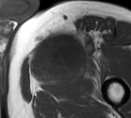
MRI of an extremity soft-tissue mass, one axial slice. Slice 51 of 55 in the series (ordered by position). MR volume resampled by the dataset authors to the PET/CT grid (not the native acquisition matrix). 131 × 118 image matrix. Male patient. From the clinical record (not read from this slice): histological type: pleiomorphic liposarcoma; grade: high; site of the primary tumour: left thigh.
Structures marked on this image (expert contour drawn on MRI and transferred to this co-registered scan by the dataset authors):
- gross tumour volume including surrounding oedema: bounding box [x1, y1, x2, y2] px = [32, 27, 97, 76]
- gross tumour volume (mass): [32, 34, 78, 70]